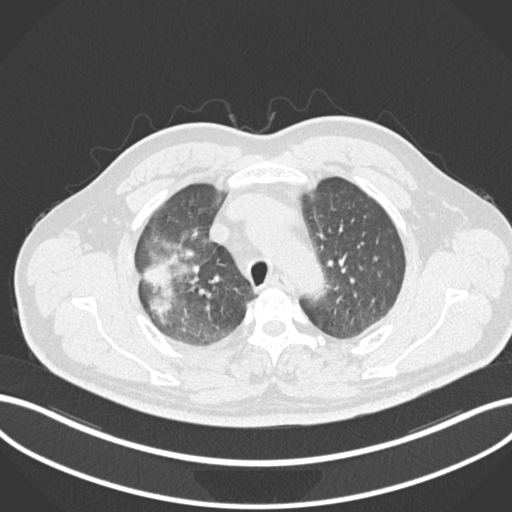
Chest CT, one axial slice; slice 680 of 852 in the series (ordered by position); reconstruction kernel B30f; lung window (W 1500 / L -600 HU); 512 × 512 image matrix. Patient: male, 55 years. Case-level facts recorded for this patient, not image findings: clinical TNM (as recorded): T3 N2 M1.
Outlined on this slice (rectangle marked by the reading radiologist):
- lung tumour (recorded histology: adenocarcinoma): bounding box <142,264,177,317> (left, top, right, bottom; pixels)